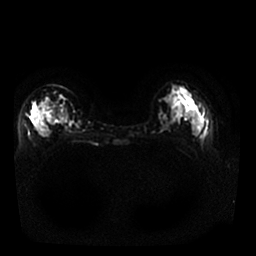
Breast MRI, one axial slice; position 9 of 25 along the scan axis; diffusion-weighted series; image 2 of 4 stored at this slice position (different b-values; order by instance number); 1.5 T; 256 × 256 image matrix, field of view 340 × 340 mm. Female patient.
Structures marked on this image (manually delineated by an expert):
- tumour on diffusion-weighted imaging: bounding box (x1, y1, x2, y2) in pixels: (33, 110, 39, 121)